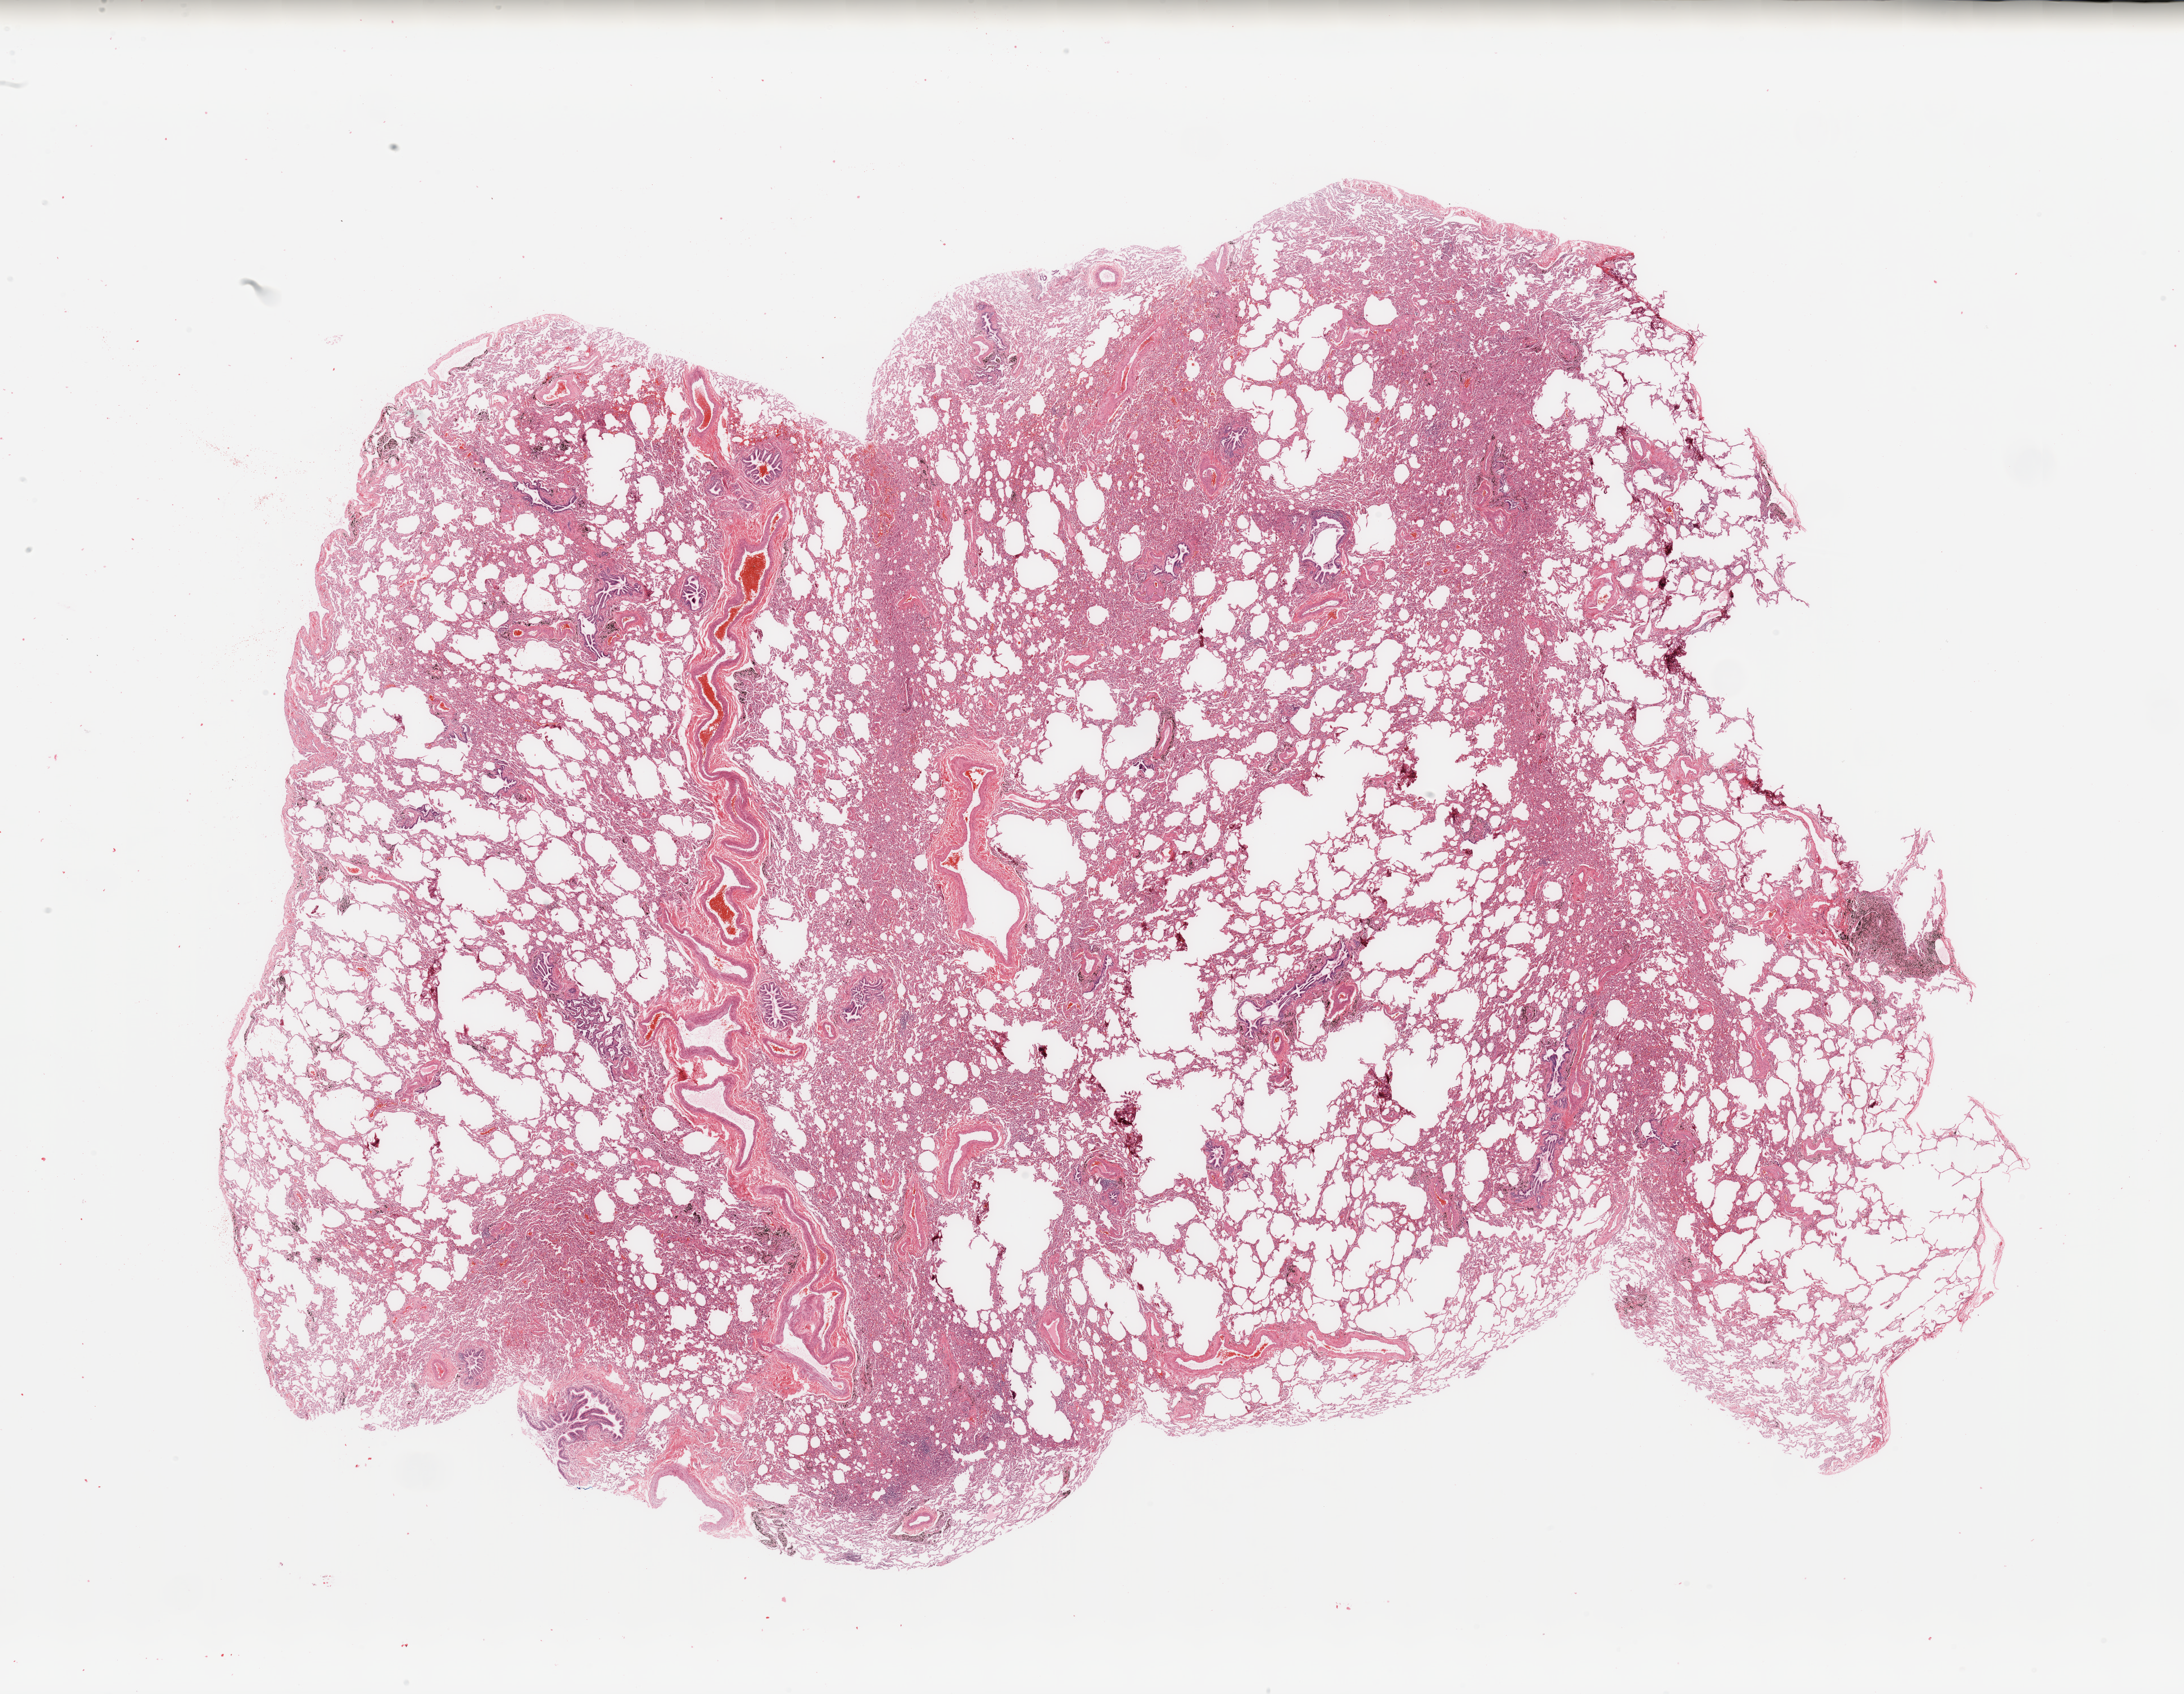
Digitized Hematoxylin and eosin (H&E) stained tissue section (whole slide) — a low-resolution overview of the entire scanned area, about 30.5 x 23.7 mm (from a 20x scan), lung, normal (non-tumour) tissue. 68-year-old female patient.
This section: normal (non-tumour) tissue from the same patient. Patient diagnosis: Adenocarcinoma, NOS.